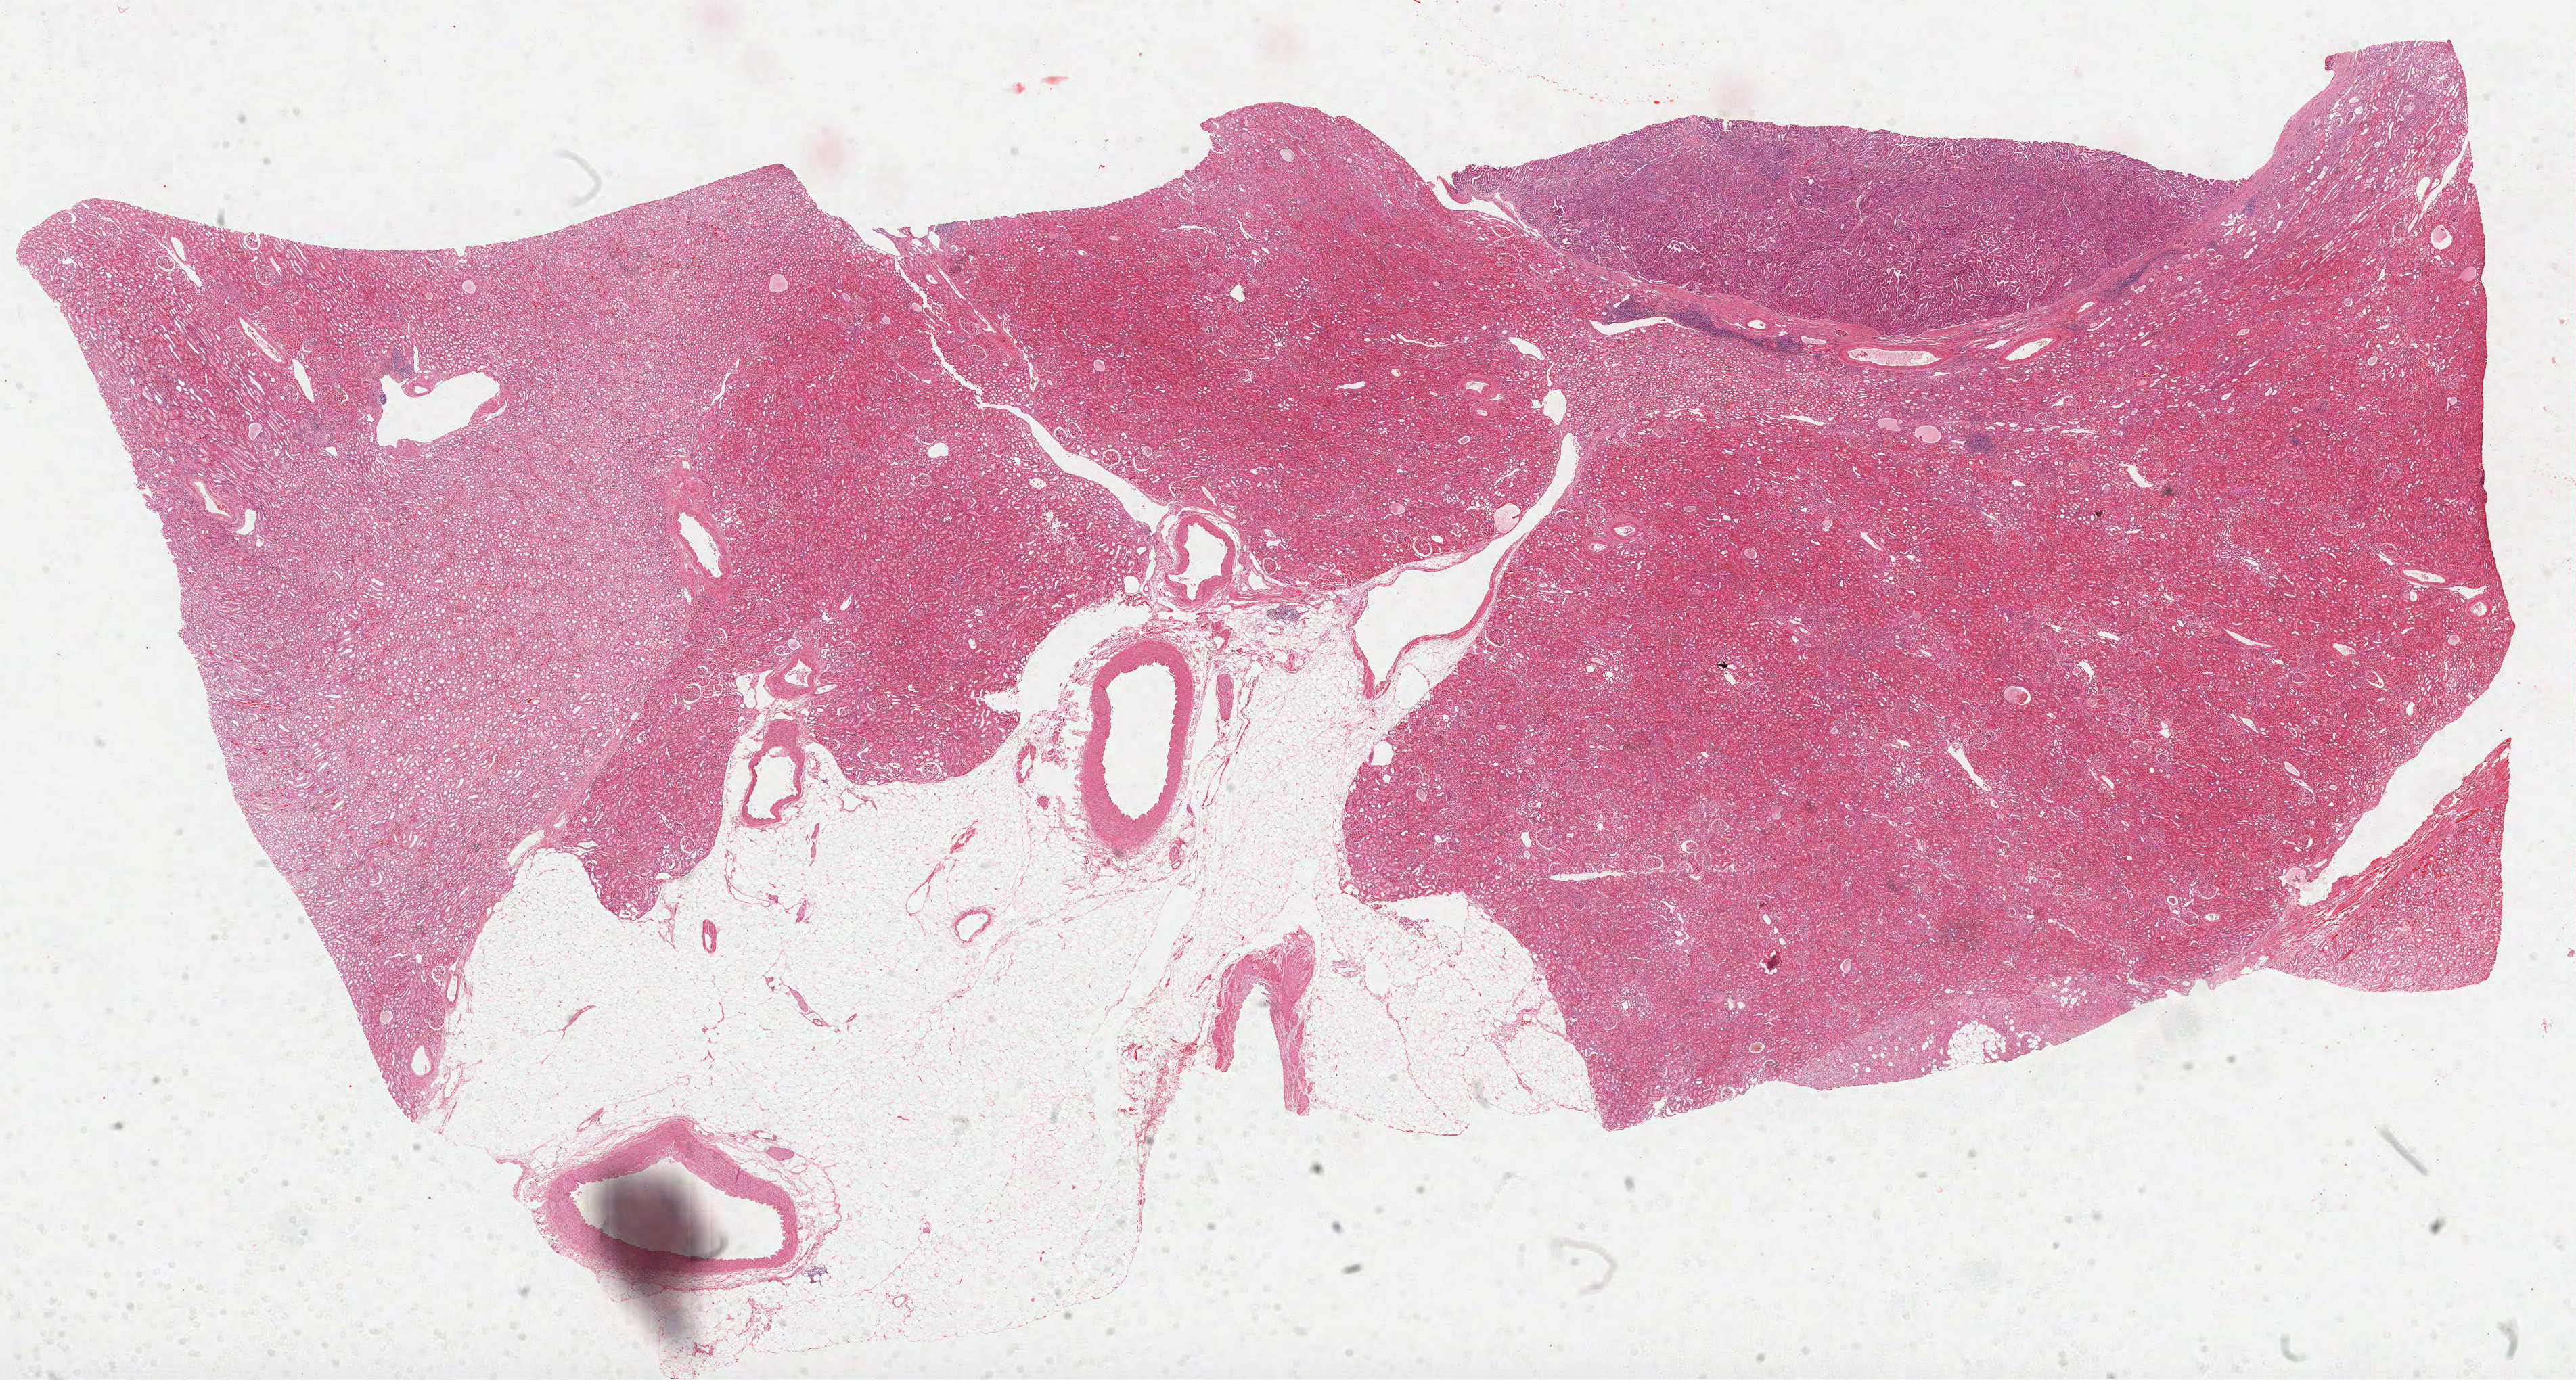
Whole-slide histology image, Hematoxylin and eosin (H&E) stained — a low-resolution overview of the entire scanned area, about 30.7 x 16.5 mm (from a 40x scan). FFPE section. Sample: primary tumour, kidney. Male patient; age at initial diagnosis 46 years.
Pathologic diagnosis: Papillary adenocarcinoma, NOS.